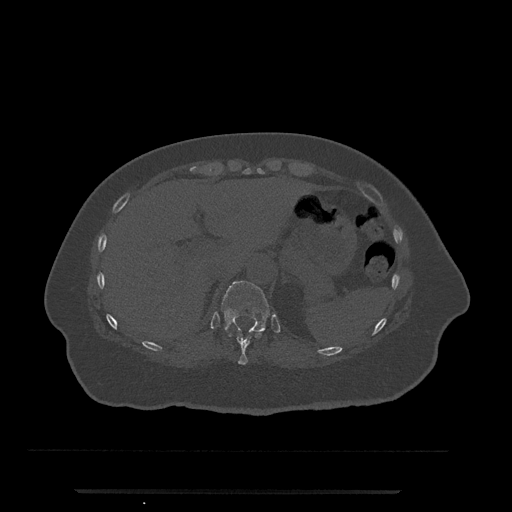
CT including the spine, one axial slice; slice 252 of 797 in the series (ordered by position); reconstruction kernel Br40s/3; bone window (W 1800 / L 400 HU); 512 × 512 image matrix. Patient: female, 51 years. Case-level facts recorded for this patient, not image findings: primary cancer: neuro; vertebrae with lytic lesions (as recorded): T8.
Annotated regions visible in this slice (semi-automatic segmentation, software-assisted and operator-edited):
- T10 vertebra: bounding box <229,330,265,365> (left, top, right, bottom; pixels)
- T11 vertebra: <221,281,270,334>